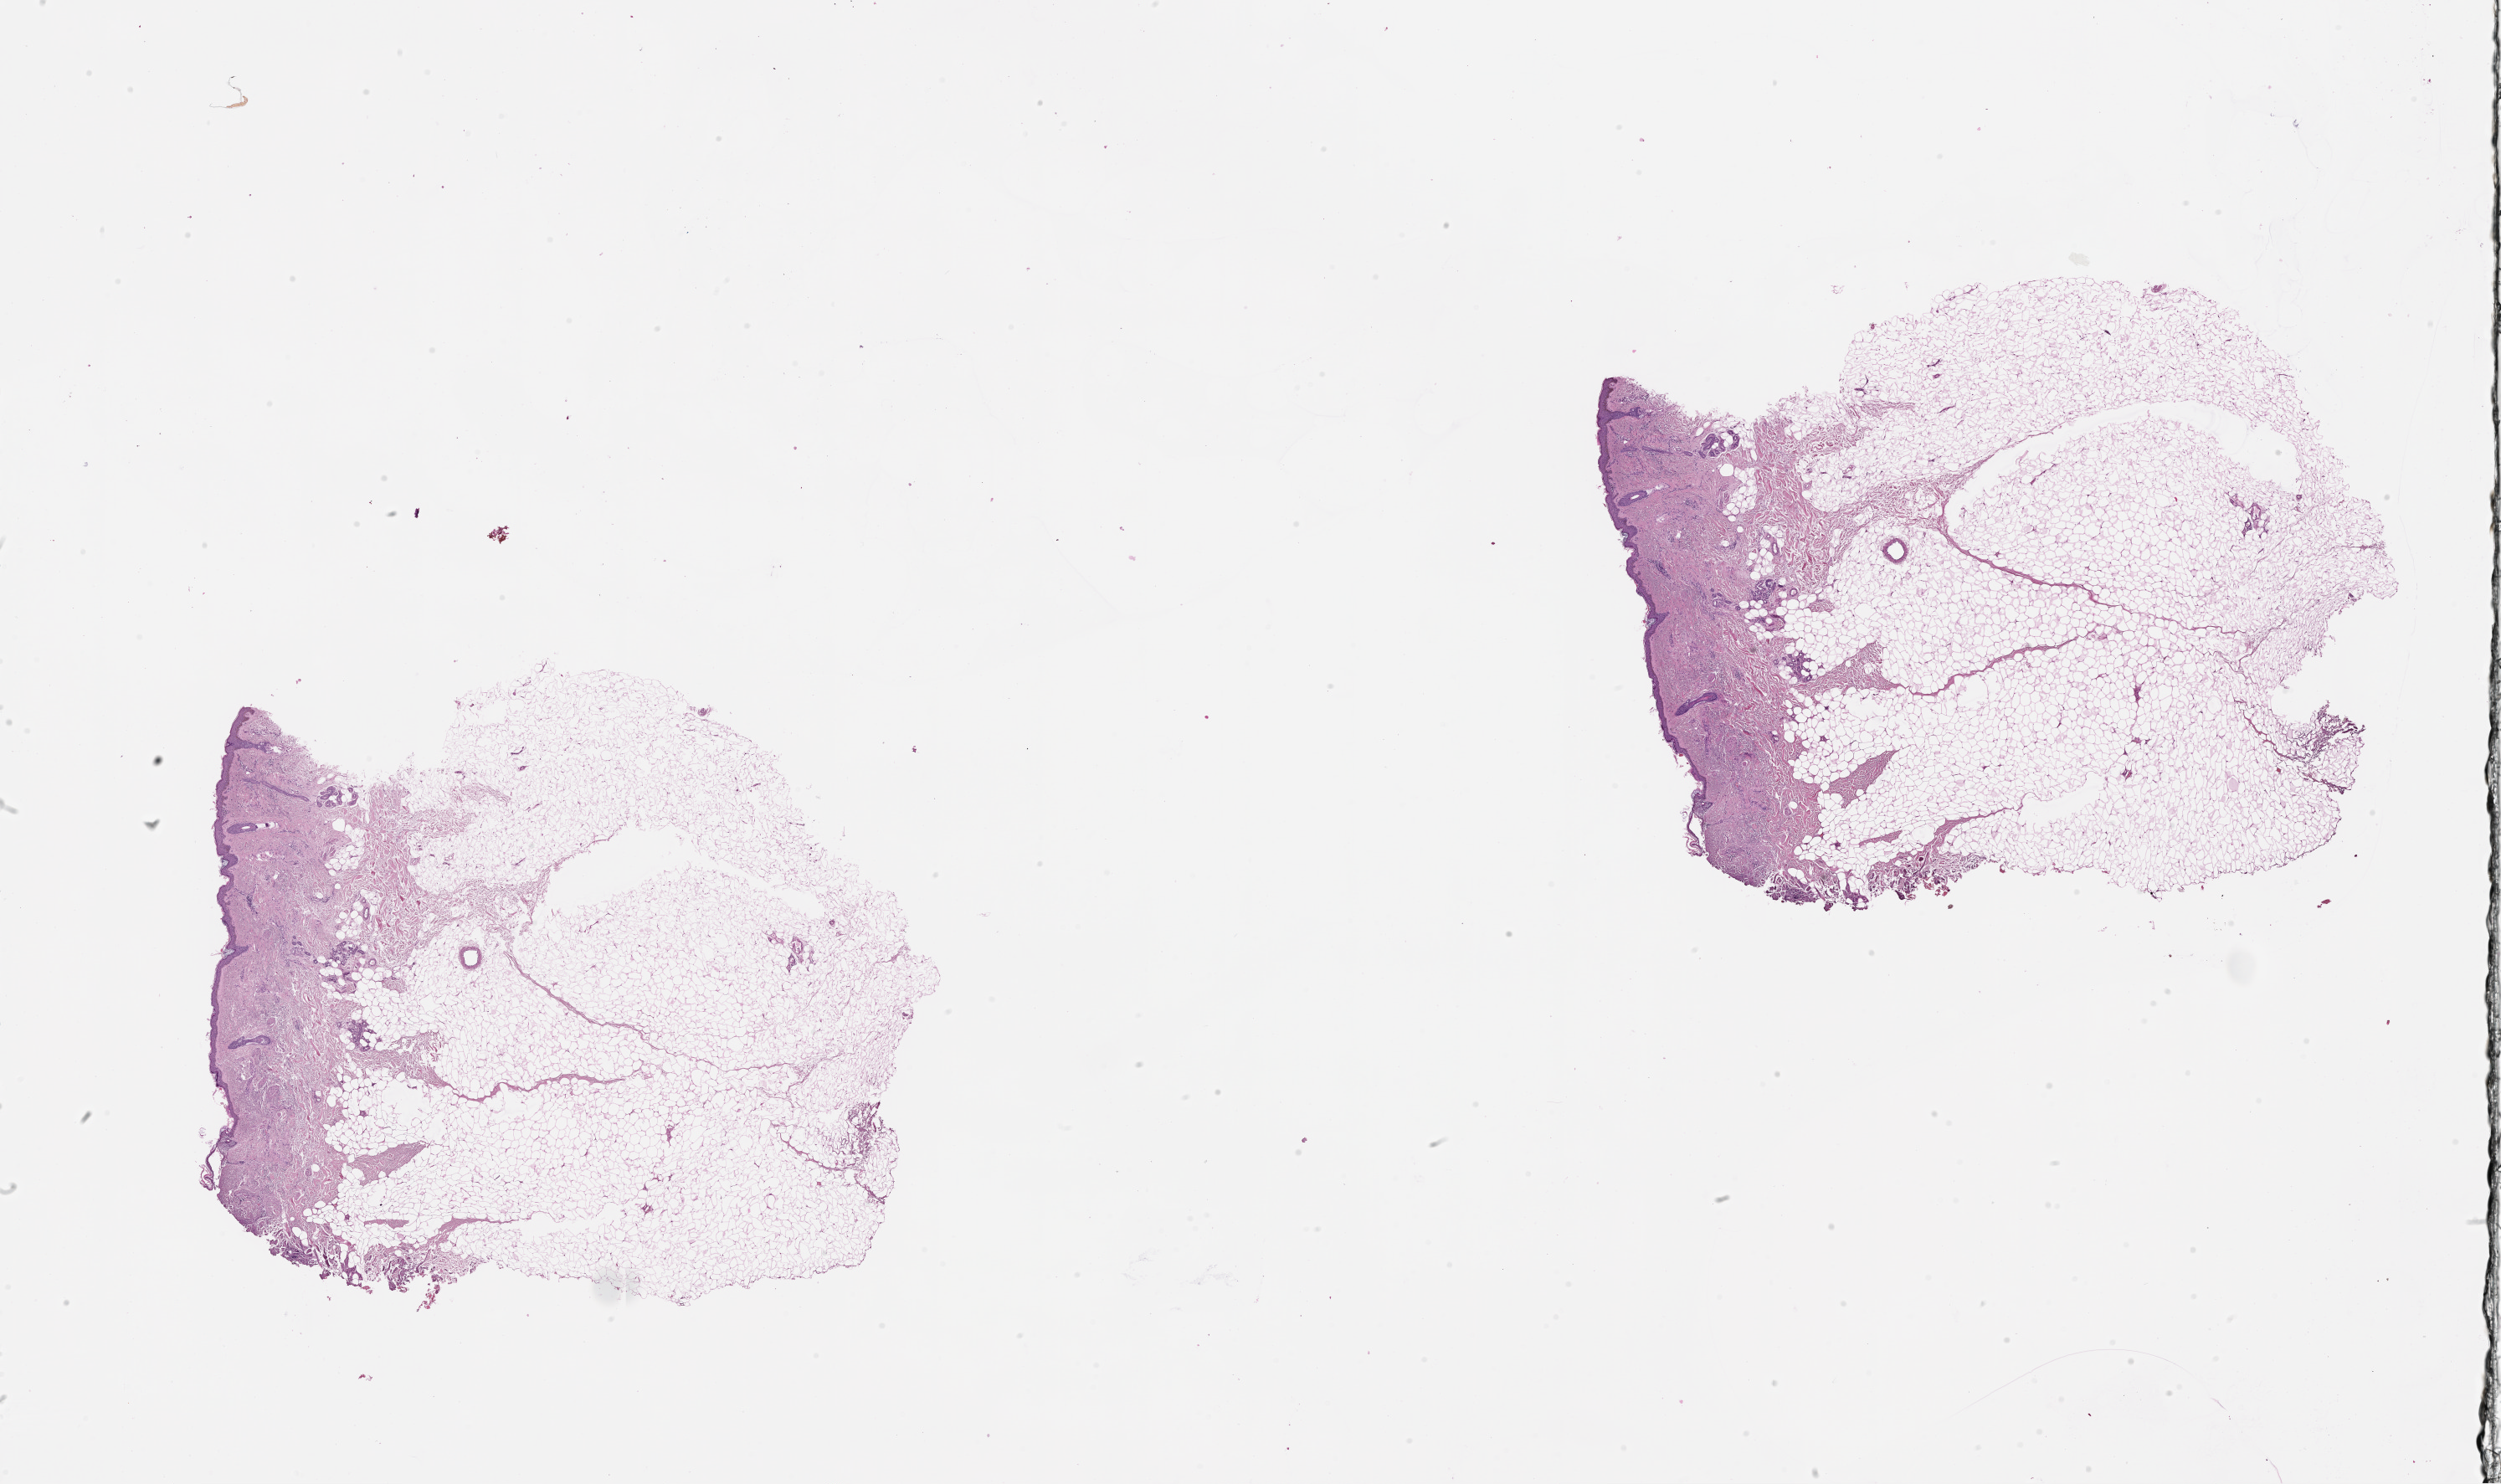
H&E whole-slide image — low-resolution overview of the scanned area, about 24.1 x 14.3 mm. 75-year-old female patient.
Patient diagnosis: Malignant melanoma, NOS.